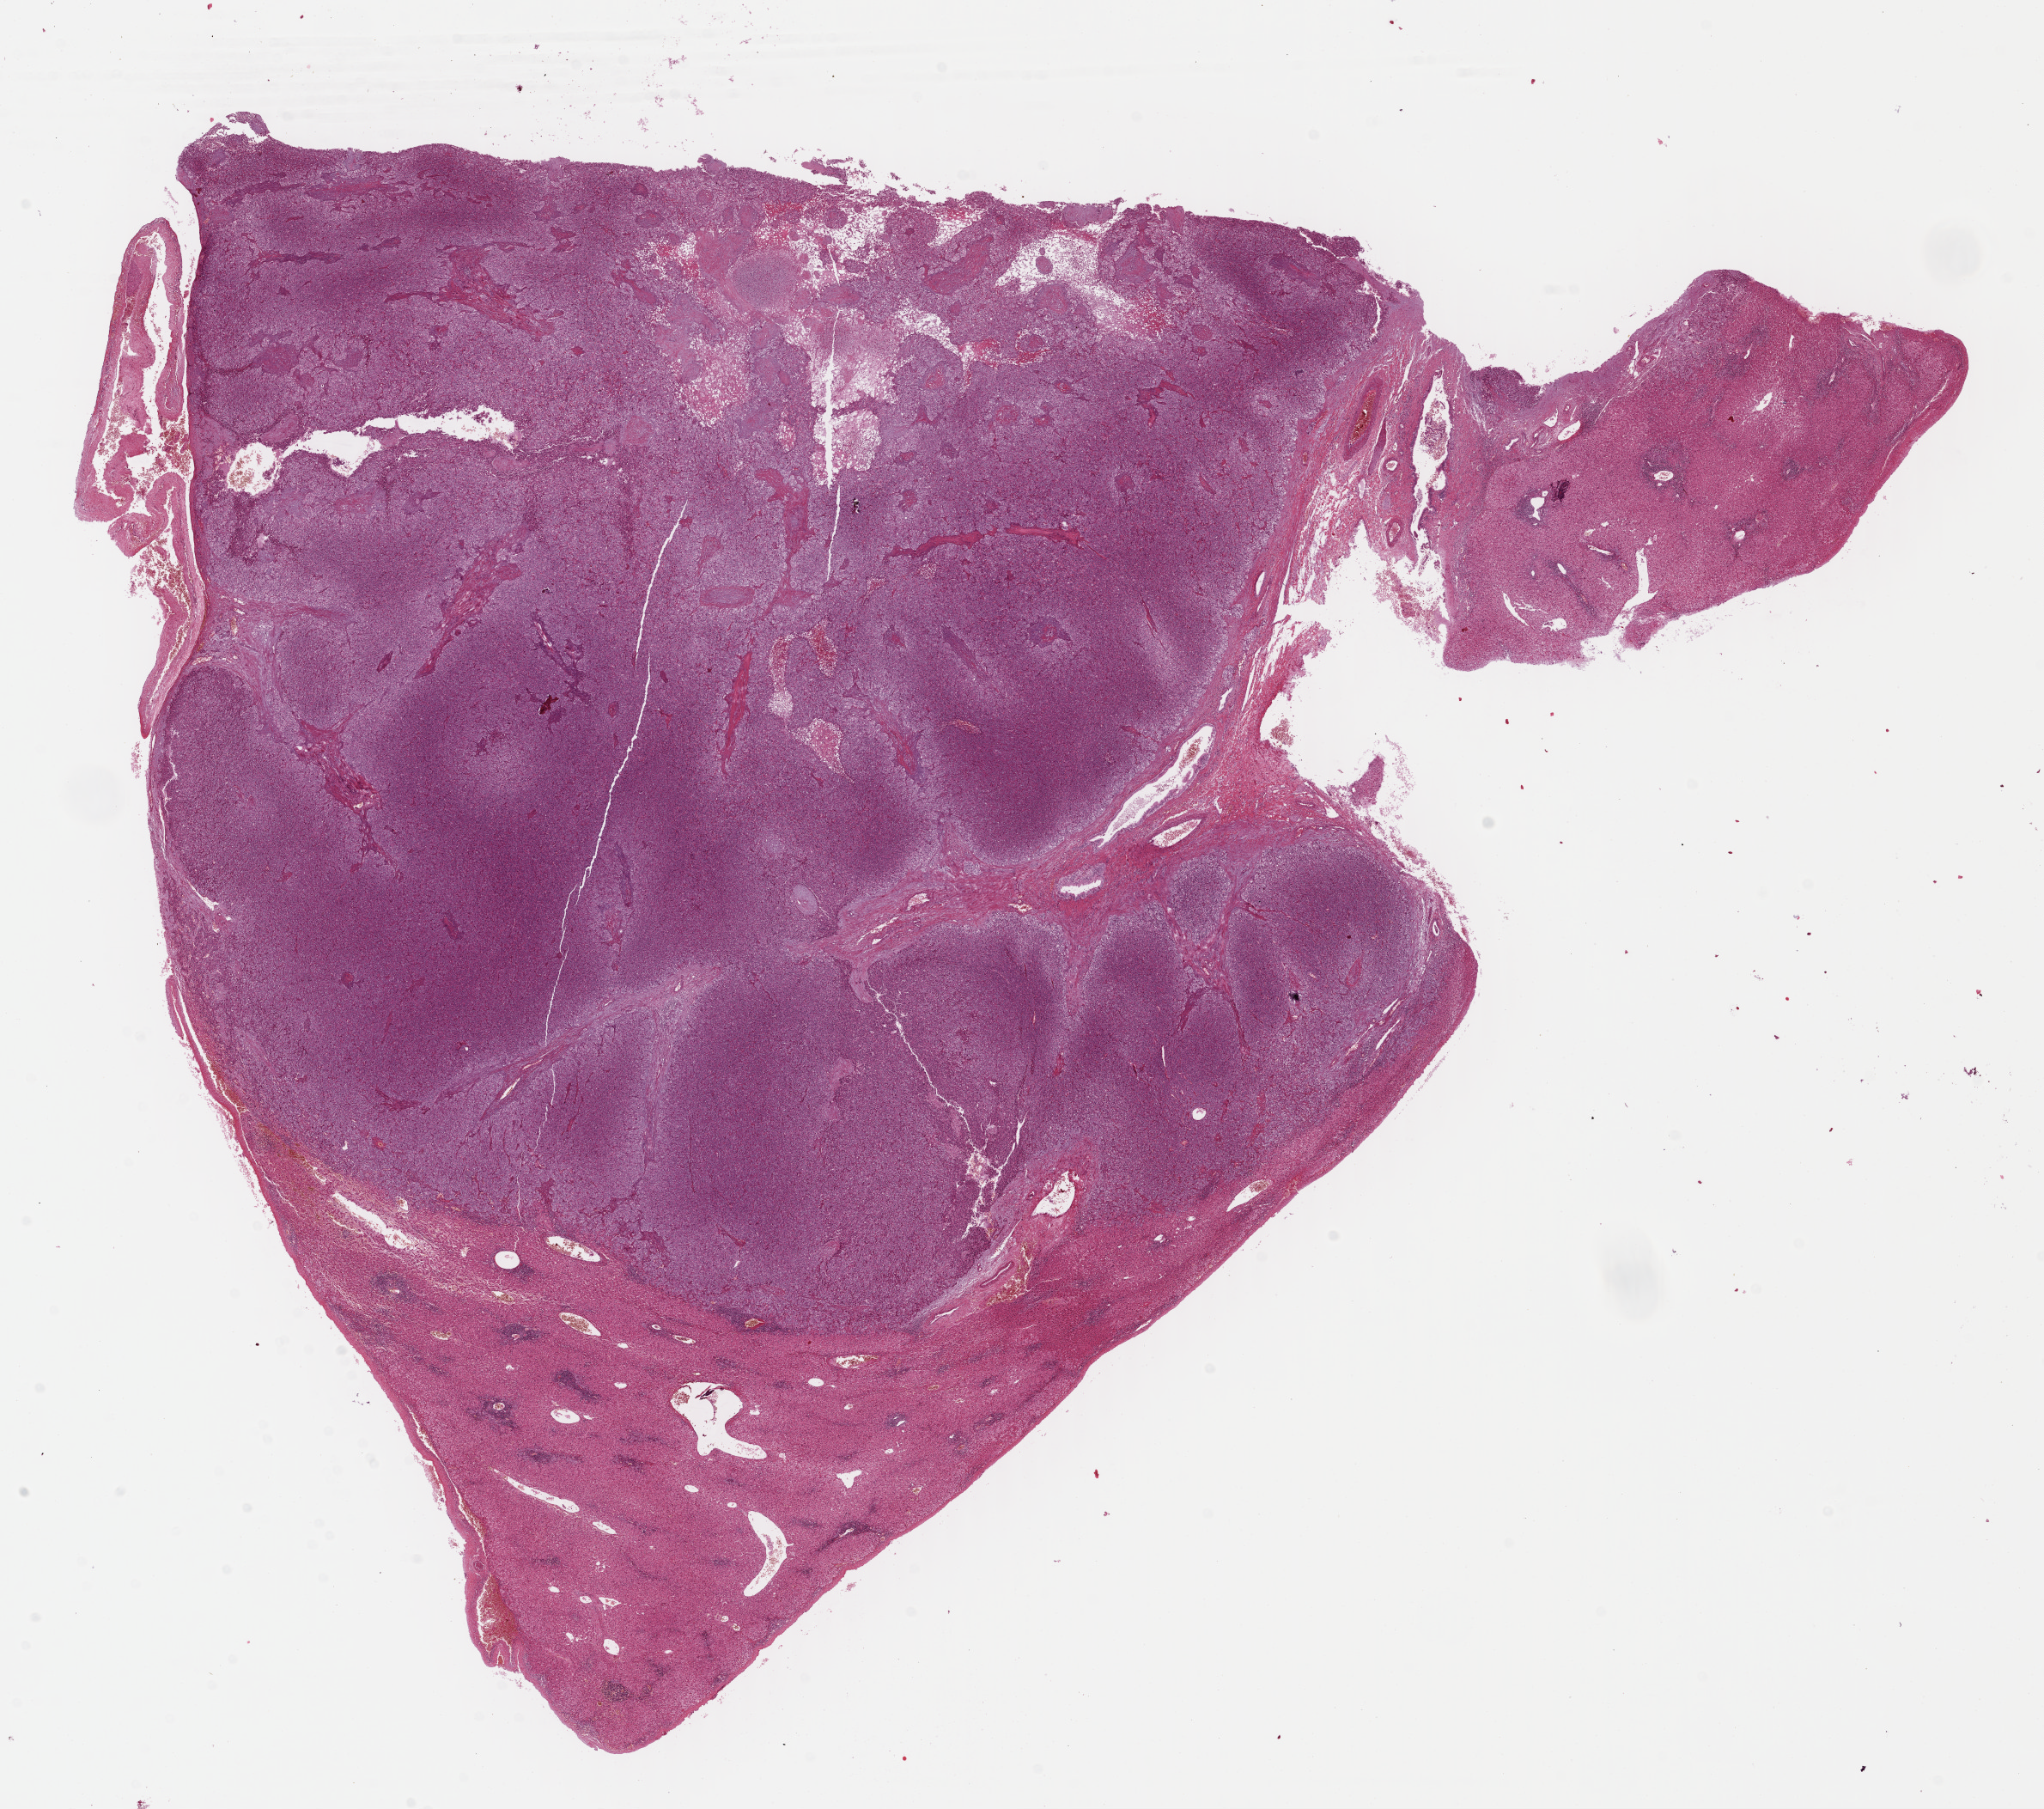
Hematoxylin and eosin (H&E) stained whole-slide image — shown as a low-resolution overview of the whole scanned area (about 18.7 x 16.6 mm, slide scanned at 40x); formalin-fixed paraffin-embedded (FFPE) diagnostic section; liver, primary tumour sample. Male, age 61 years at initial diagnosis. Histologic grade: G2 (moderately differentiated).
- AJCC pathologic stage: IIIA (7th edition)
- pathologic diagnosis: Hepatocellular carcinoma, NOS